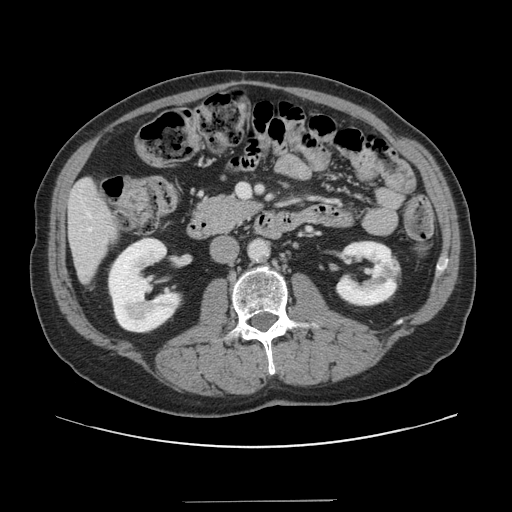
Contrast-enhanced abdominal CT, one axial slice; slice 48 of 151 in the series (ordered by position); 120 kVp; intravenous contrast given; soft-tissue window (W 400 / L 40 HU); 2.5 mm slice thickness; 512 × 512 image matrix, field of view 399 × 399 mm. Male patient, age 63 years. Case-level facts recorded for this patient, not image findings: diagnosis: colorectal cancer liver metastases, imaged before liver resection; multiple liver metastases: no; largest metastasis: 2.1 cm.
Outlined on this slice (expert manual segmentation):
- liver: box from (x=69, y=180) to (x=117, y=281) px
- planned liver remnant (the part of the liver to remain after resection): (x=69, y=180)–(x=118, y=281)
- portal vein (with intrahepatic branches): (x=238, y=184)–(x=250, y=197)